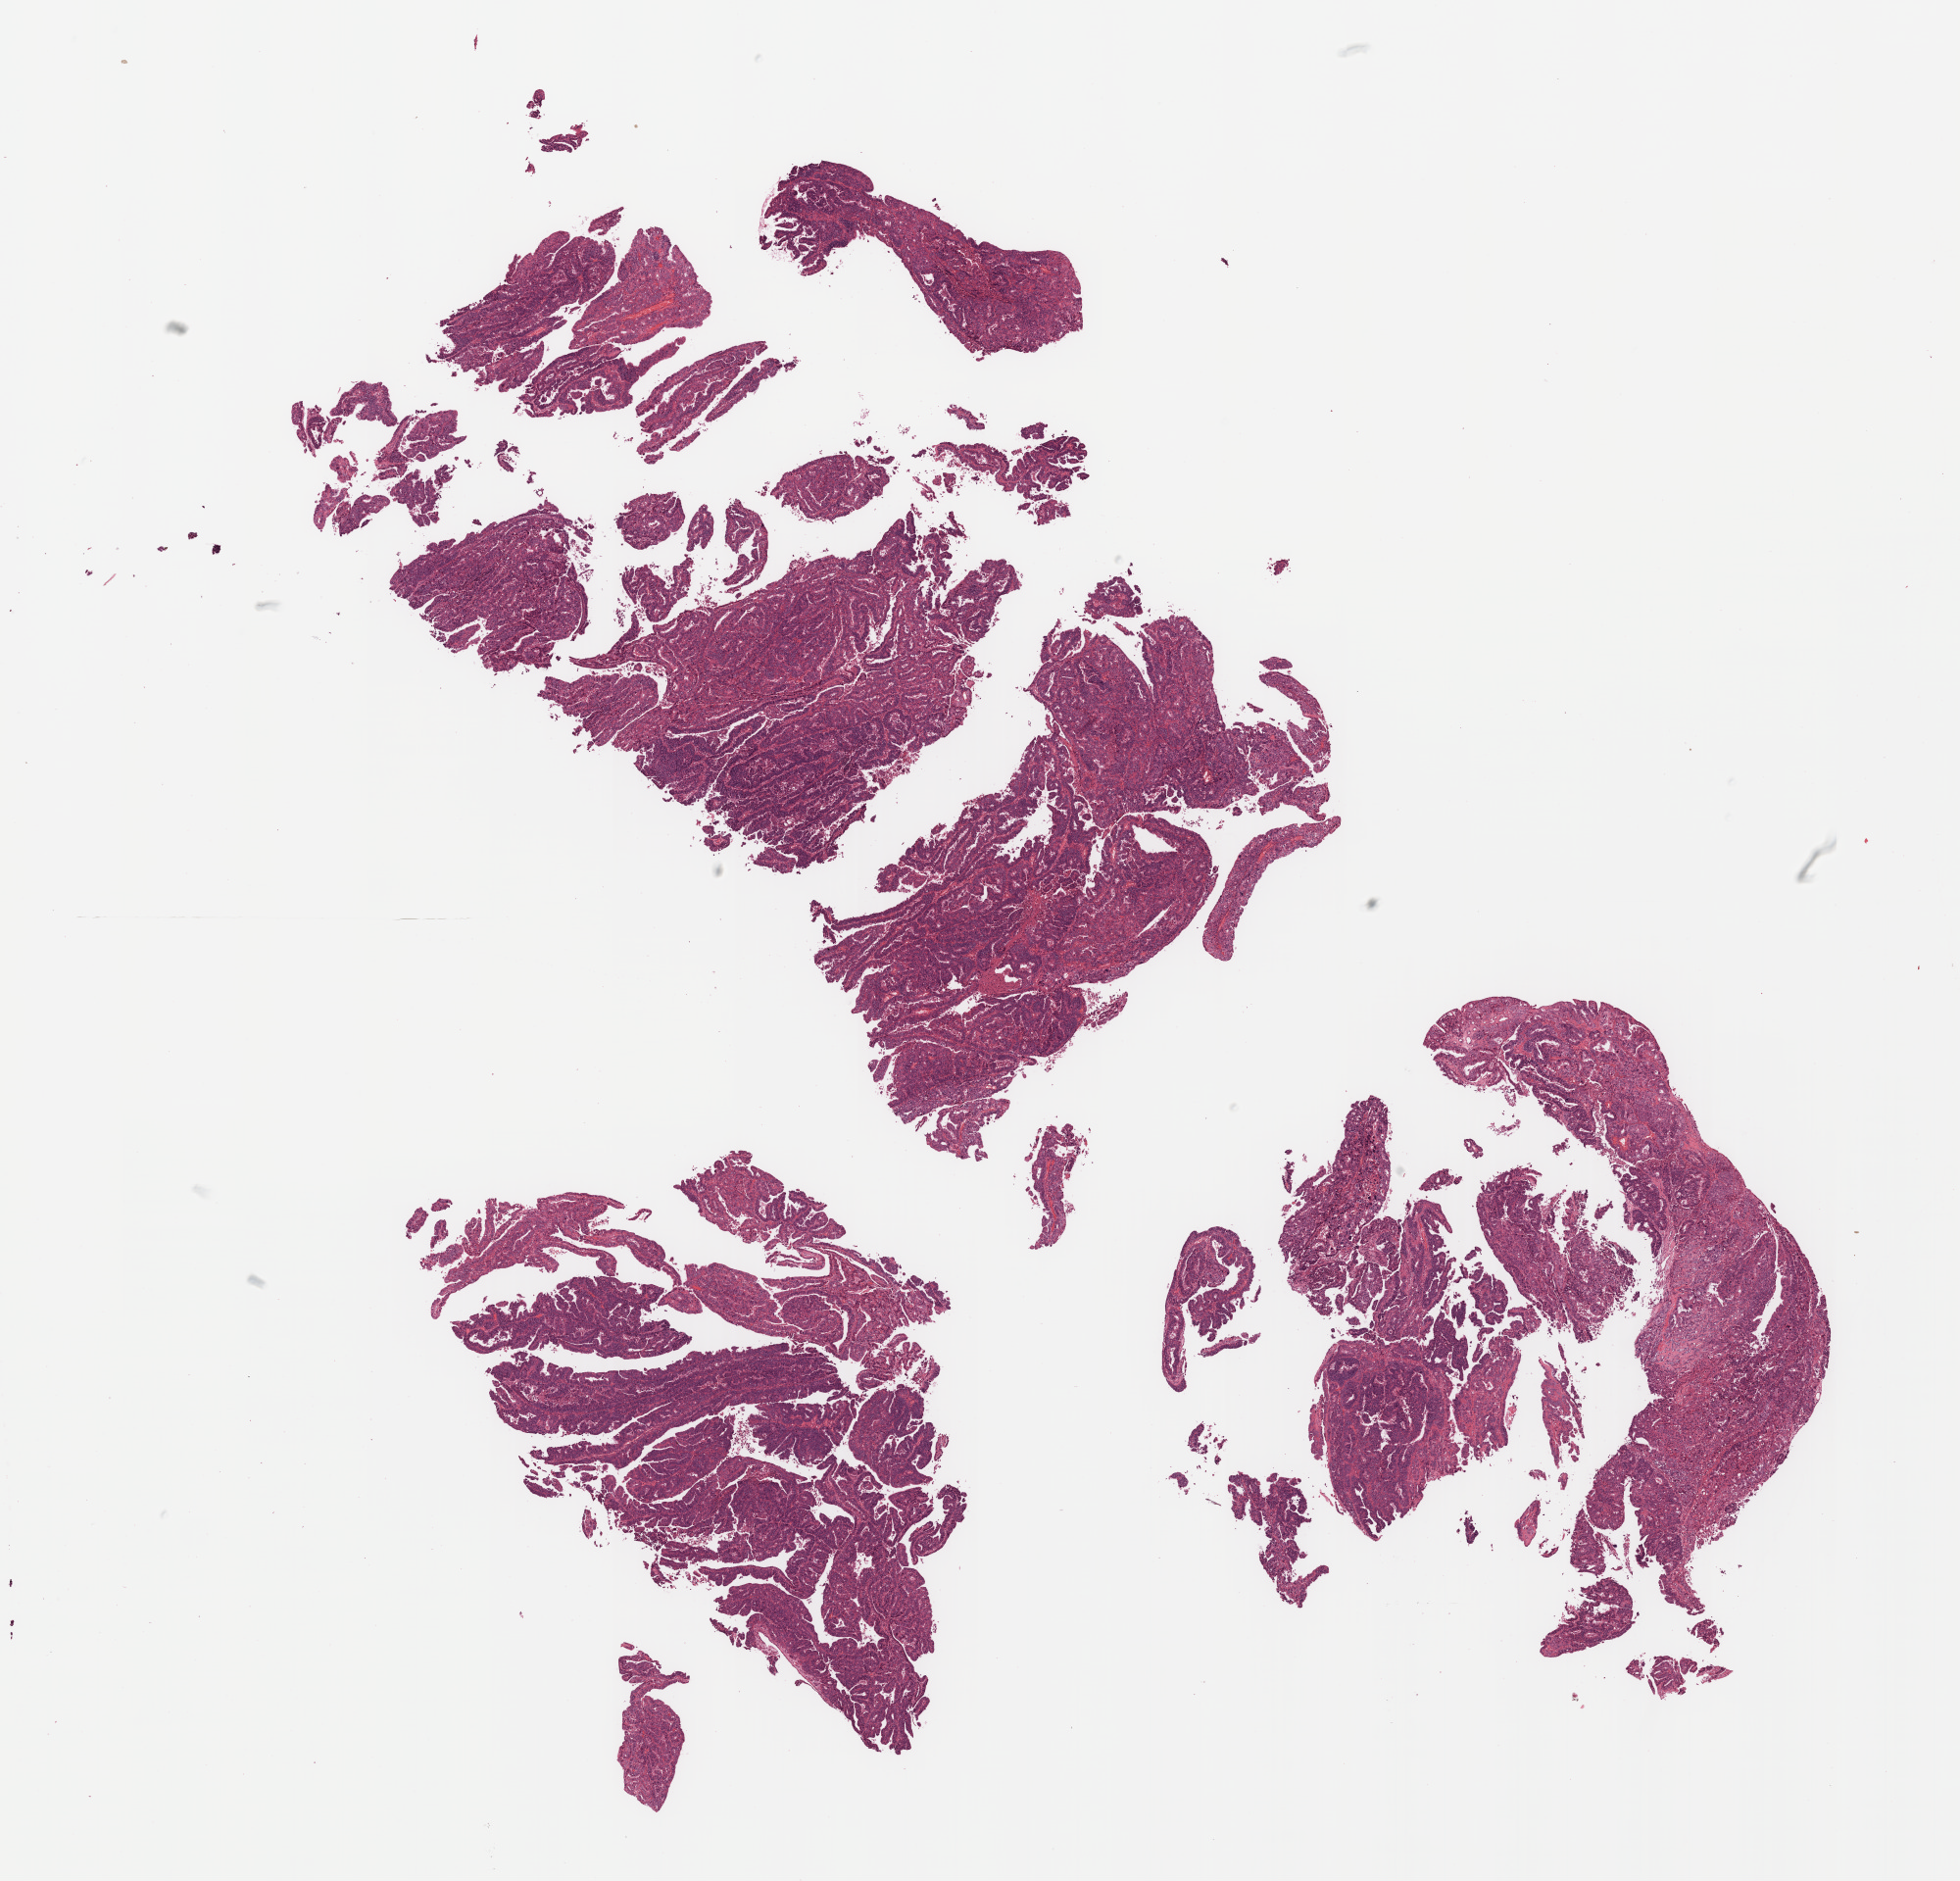
Digitized H&E-stained tissue section (whole slide), whole scanned area (about 16.0 x 15.4 mm) shown as a low-resolution overview; formalin-fixed paraffin-embedded (FFPE) diagnostic section; uterus, primary tumour sample. Patient: female, age at initial diagnosis 73 years. Histologic grade: G3 (poorly differentiated).
* FIGO stage: IVB
* histologic diagnosis: Serous cystadenocarcinoma, NOS (endometrium)